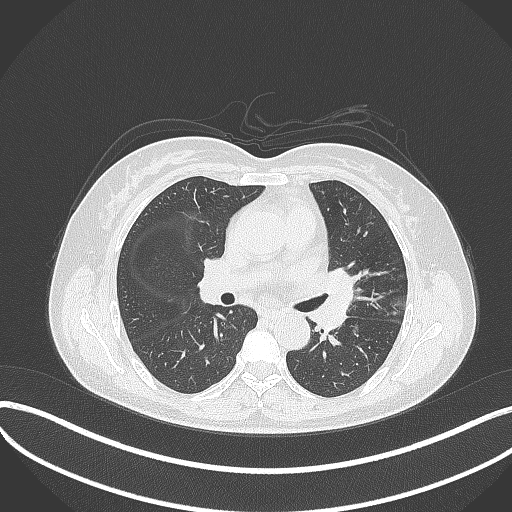
Chest CT, one axial slice. Reconstruction kernel B70f. Lung window (W 1500 / L -600 HU). 1 mm slice thickness. 512 × 512 image matrix. Patient: female, 54 years. Case-level facts recorded for this patient, not image findings: clinical TNM (as recorded): T2a N1 M0; histopathological grade: G3.
Annotated regions visible in this slice (rectangle marked by the reading radiologist):
- lung tumour (recorded histology: small cell carcinoma): bounding box (x1, y1, x2, y2) in pixels: (311, 266, 354, 337)